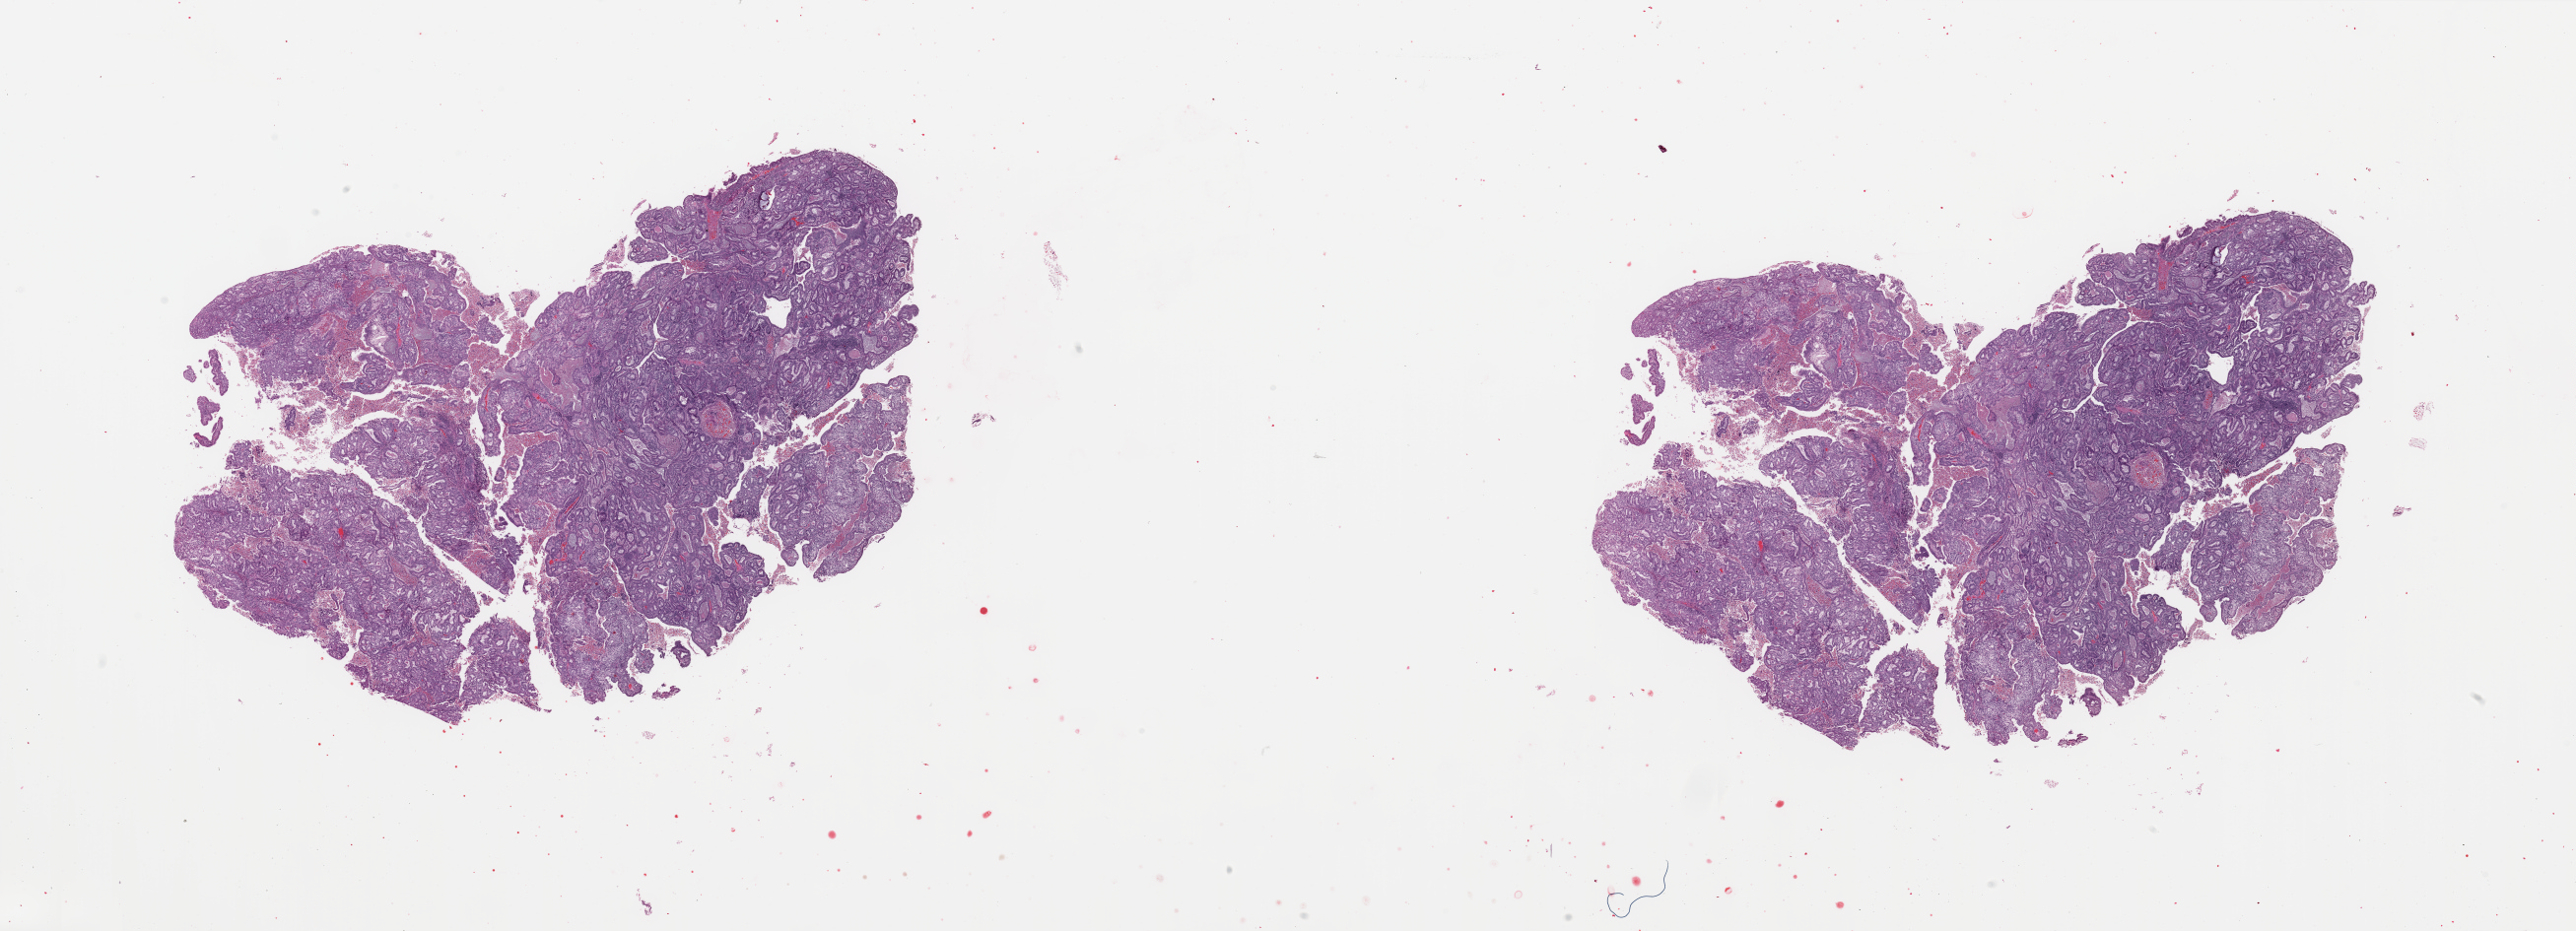
H&E-stained whole-slide image — low-resolution overview of the scanned area, about 41.3 x 14.9 mm (acquisition: 20x scan), uterus, tumour tissue. 72-year-old female patient. Histologic grade: G2 (moderately differentiated).
AJCC pathologic stage: I. Diagnosis: Endometrioid adenocarcinoma, NOS.